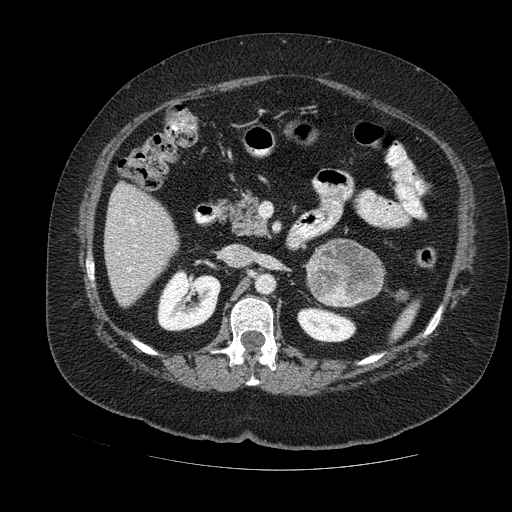
Contrast-enhanced abdominal CT, one axial slice. Slice 63 of 121 in the series (ordered by position). Soft-tissue window (W 400 / L 40 HU). 512 × 512 image matrix. Female patient. From the clinical record (not read from this slice): diagnosis: adrenocortical carcinoma; tumour side: left adrenal; tumour size at pathology: 8 cm; Ki-67 index: 7 %; stage (as recorded): 2.
Outlined on this slice (semi-automatic segmentation, software-assisted and operator-edited):
- mass: box from (x=307, y=241) to (x=382, y=309) px